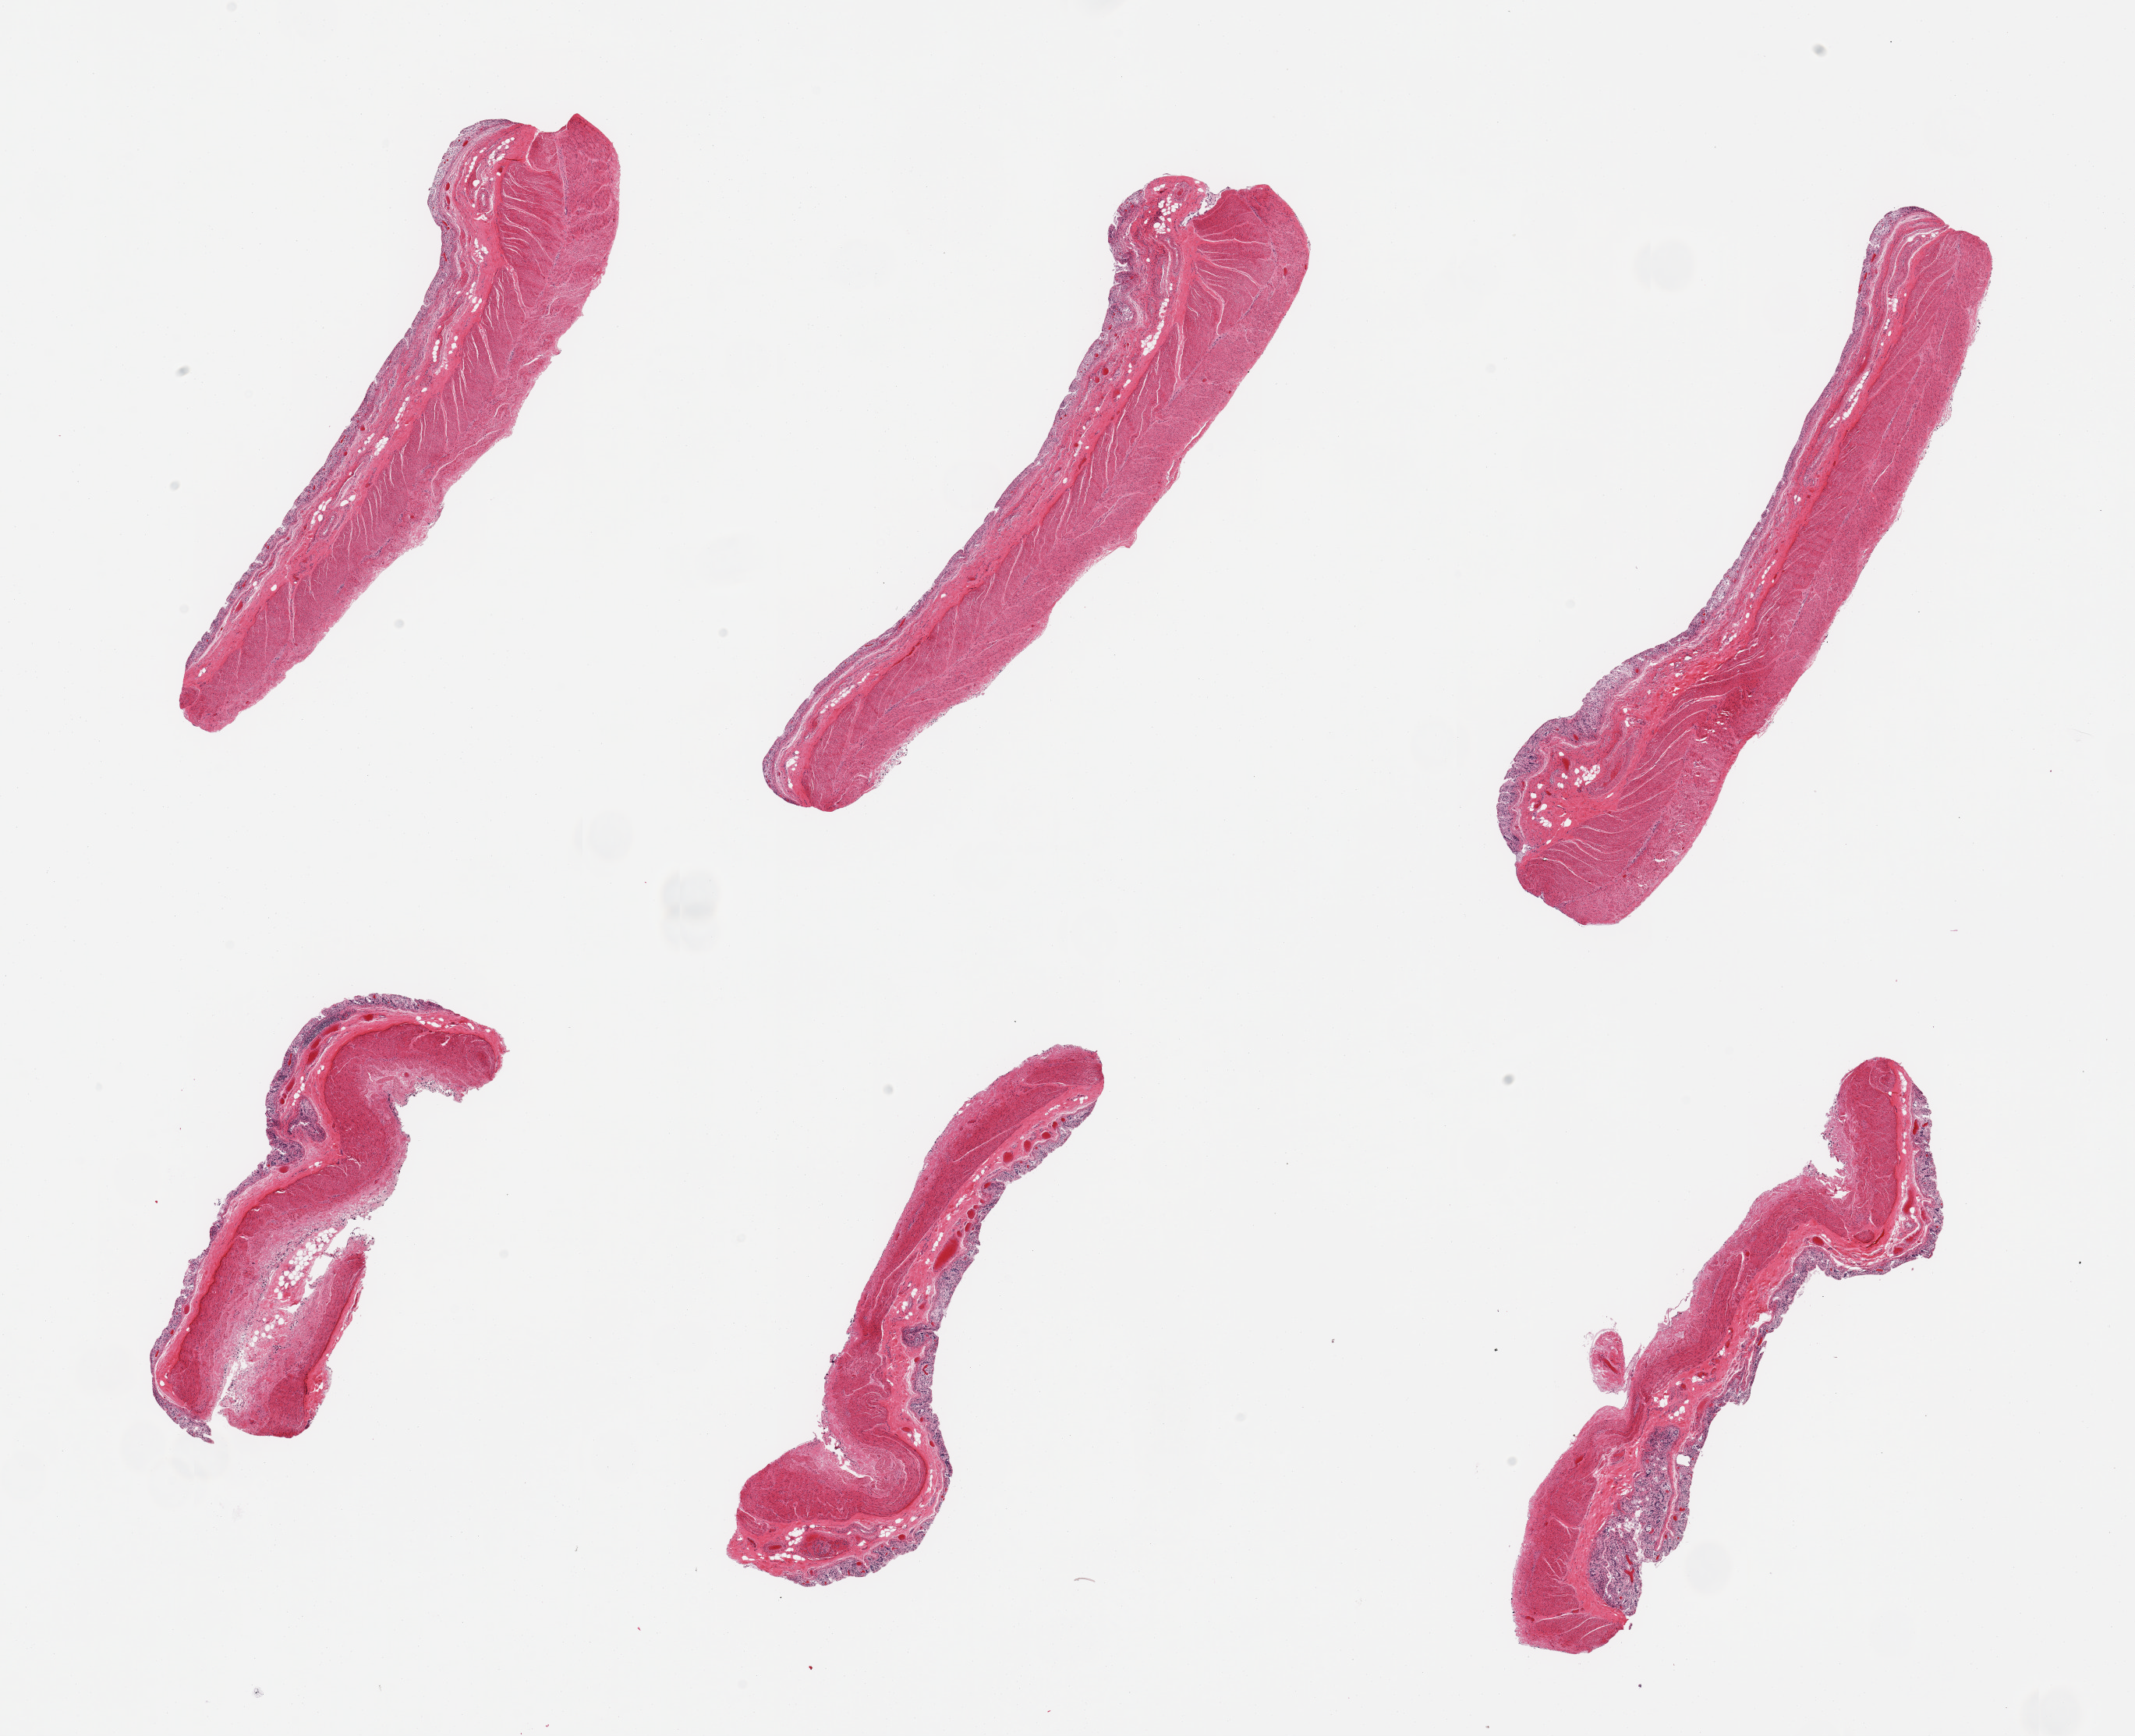
Haematoxylin and eosin whole-slide image, brightfield, shown as a low-resolution overview of the whole scanned area (about 21.7 x 17.6 mm); PAXgene-fixed paraffin-embedded (PFPE) section; section of transverse colon (target tissue); donor tissue sample. Donor sex: female.
Review note (as recorded): 6 pieces; mucosa totally necrotic; muscle intact.